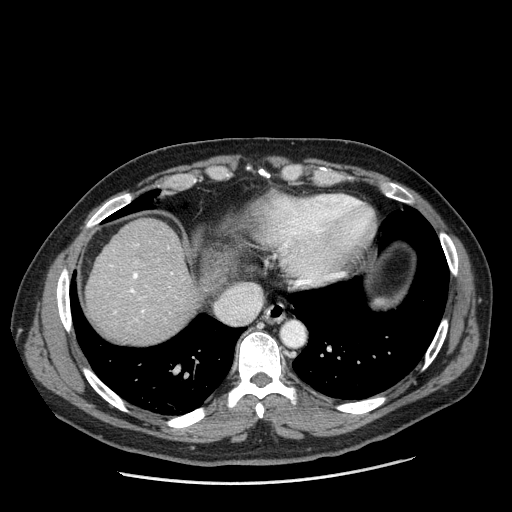
Contrast-enhanced abdominal CT (liver protocol), one axial slice; reconstruction kernel STANDARD; 120 kVp; one of 2 acquisitions stored at this slice position; soft-tissue window (W 400 / L 40 HU); 2.5 mm slice thickness; 512 × 512 image matrix, field of view 400 × 400 mm. Case-level facts recorded for this patient, not image findings: diagnosis: hepatocellular carcinoma (patient treated with transarterial chemoembolisation; whether this scan precedes or follows treatment is not stated here); TNM stage (as recorded): Stage-II; Child-Pugh class: A; tumour size: 2.6 cm.
Outlined on this slice (semi-automatic segmentation, software-assisted and operator-edited):
- abdominal aorta: box from (x=283, y=322) to (x=304, y=345) px
- liver parenchyma outside the tumour (the mass and vessels are separate outlines, so this box may not span the whole liver): (x=86, y=218)–(x=198, y=344)
- liver vessels: (x=115, y=244)–(x=173, y=313)